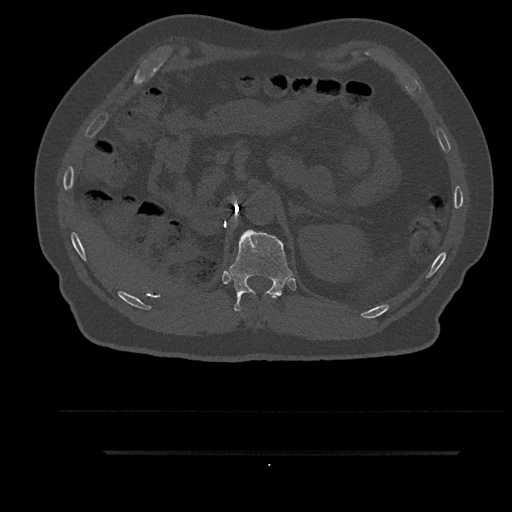
CT including the spine, one axial slice. Slice 256 of 797 in the series (ordered by position). 120 kVp. Bone window (W 1800 / L 400 HU). 0.5 mm slice thickness. 512 × 512 image matrix. Patient: male, 63 years. From the clinical record (not read from this slice): primary cancer: renal.
Annotated regions visible in this slice (semi-automatic segmentation, software-assisted and operator-edited):
- T11 vertebra: bounding box <272,296,278,298> (left, top, right, bottom; pixels)
- T12 vertebra: <227,230,294,311>